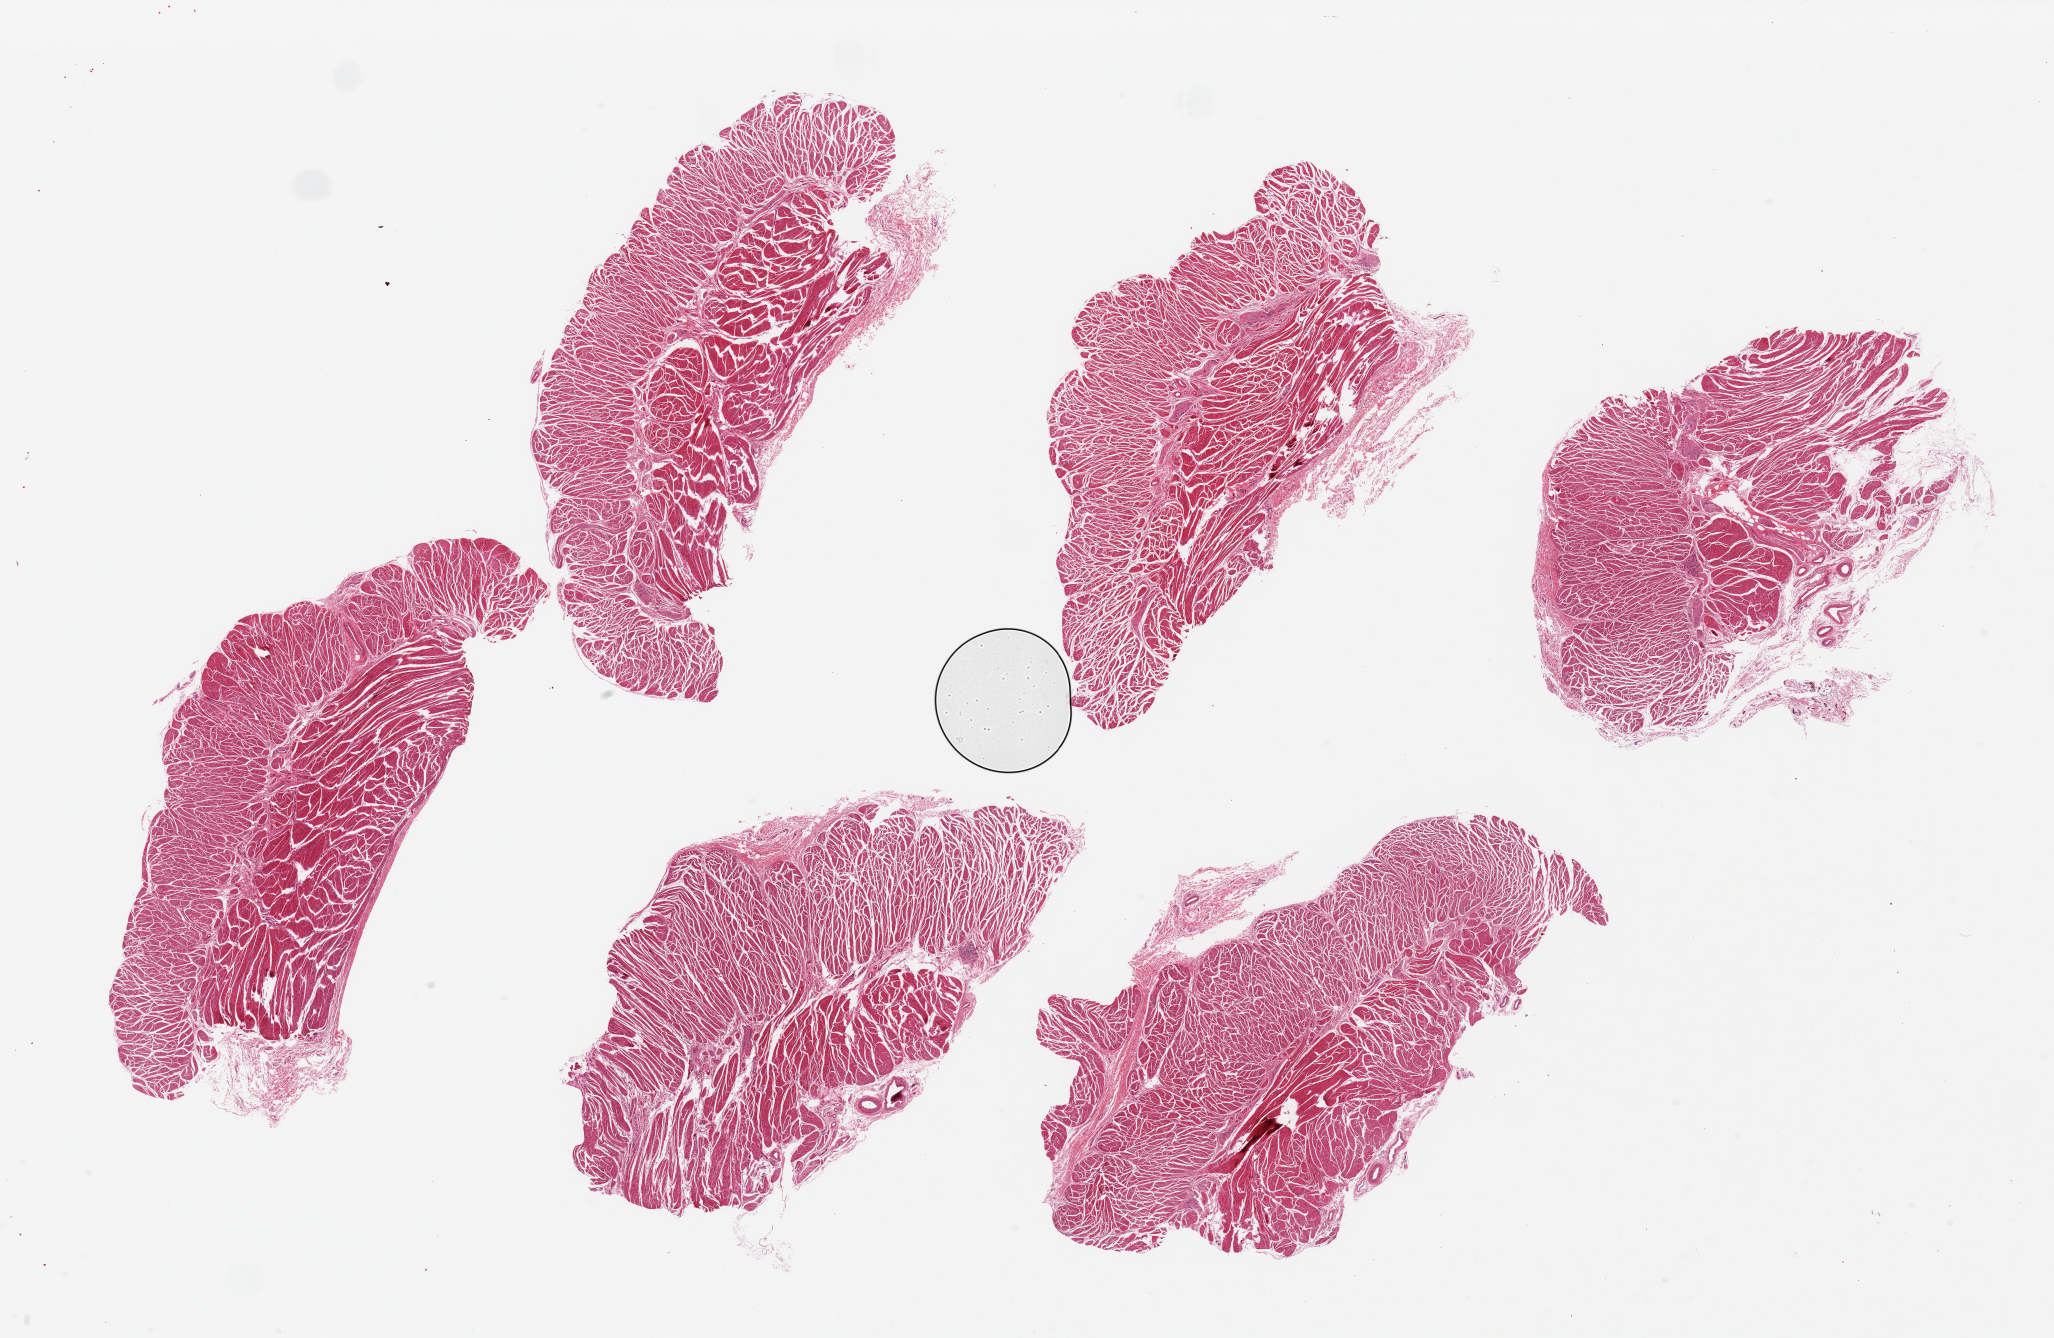
Digitized hematoxylin and eosin (H&E)-stained section, brightfield — low-resolution overview of the scanned area, about 32.5 x 21.2 mm (from a 20x scan). PAXgene-fixed paraffin-embedded (PFPE) section. Section of gastroesophageal junction (target tissue). Tissue donor sample.
Pathologist's review note for this sample: 6 6pieces ~9x3mm, all muscle, no muscosa.